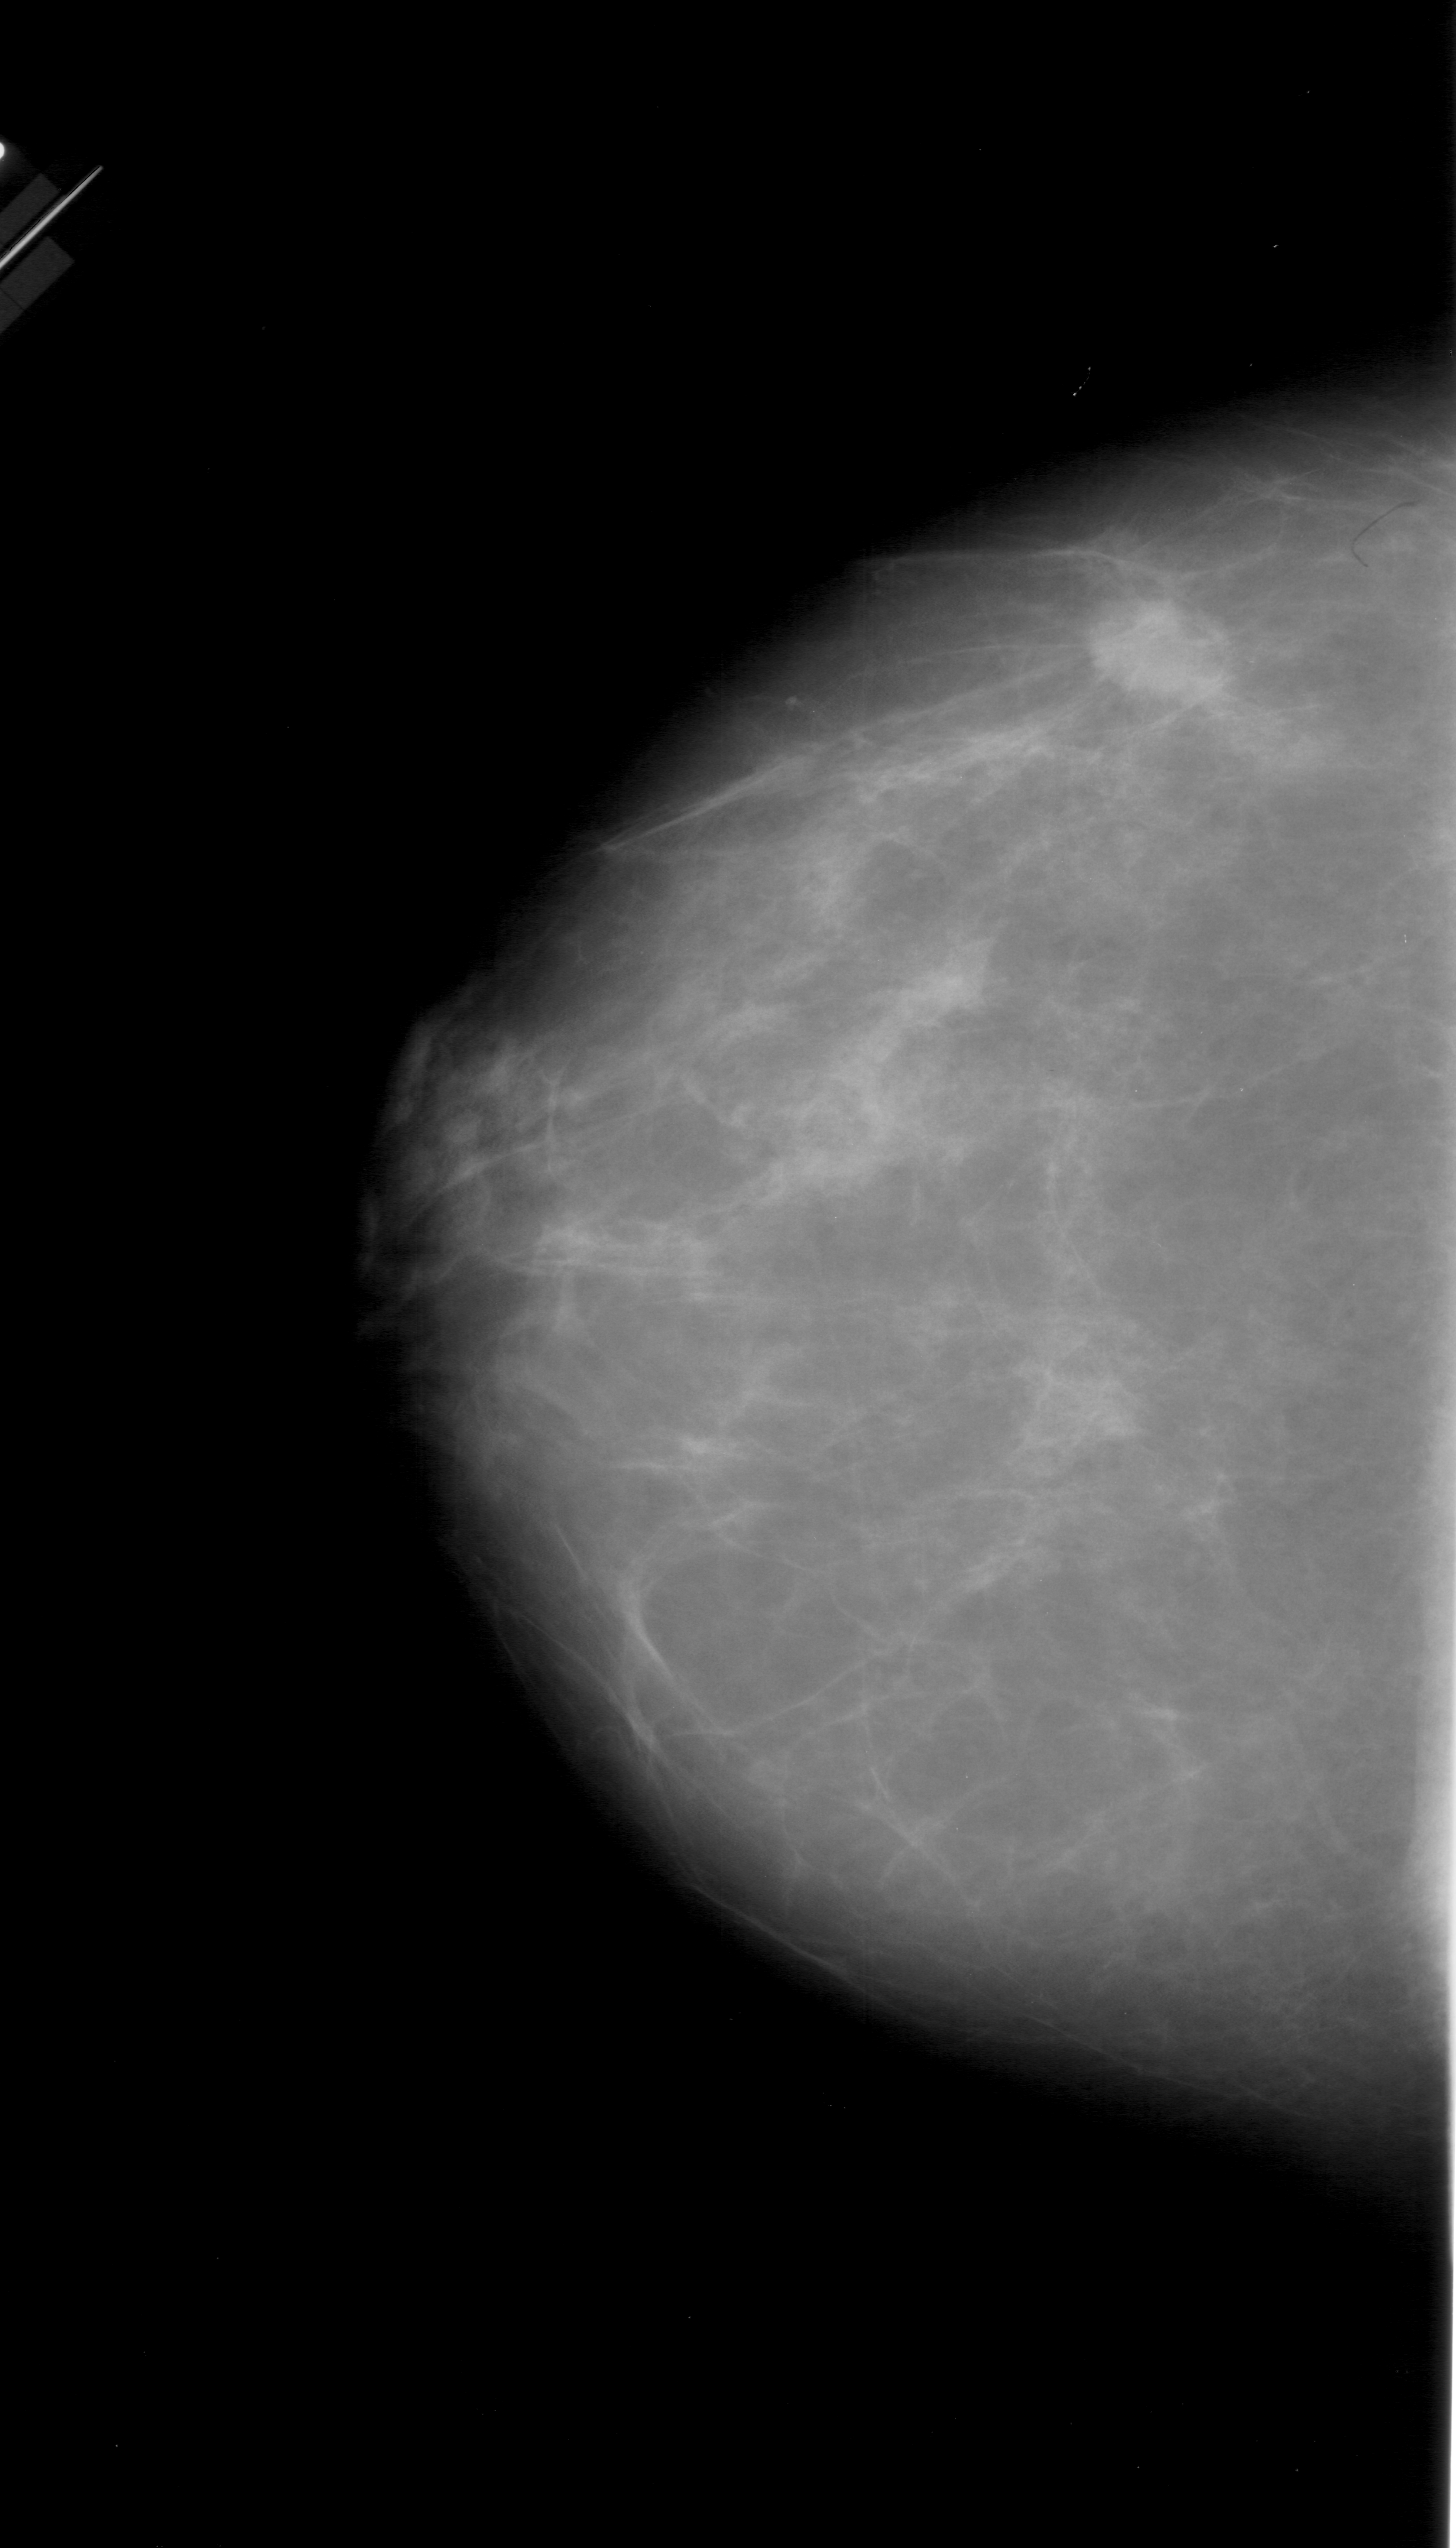
Digitized screen-film mammogram, left breast, CC view, breast composition: scattered fibroglandular densities (BI-RADS density category 2 of 4).
Finding: mass, shape irregular, margins spiculated; BI-RADS assessment category 5; pathology result (as recorded, not read from the image): malignant.